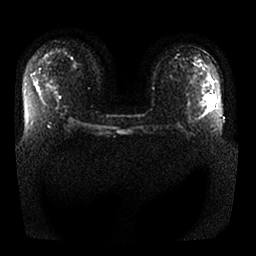
Breast MRI, one axial slice; slice 17 of 25 in the series (ordered by position); diffusion-weighted series; image 2 of 4 stored at this slice position (different b-values; order by instance number); 1.5 T; 256 × 256 image matrix, field of view 360 × 360 mm. Female patient.
Structures marked on this image (expert manual segmentation):
- tumour on diffusion-weighted imaging: bounding box (x1, y1, x2, y2) in pixels: (206, 95, 216, 103)